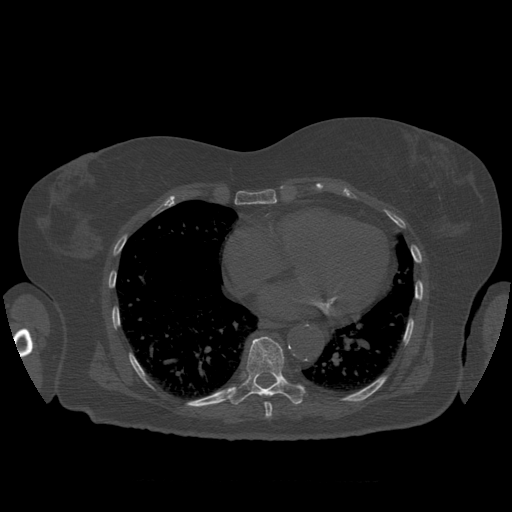
CT including the spine, one axial slice; position 363 of 399 along the scan axis; reconstruction kernel STANDARD; bone window (W 1800 / L 400 HU); 1.25 mm slice thickness; 512 × 512 image matrix, field of view 404 × 404 mm. Patient age 81 years. From the clinical record (not read from this slice): primary cancer: renal; vertebrae with lytic lesions (as recorded): L1.
Structures marked on this image (semi-automatic segmentation, software-assisted and operator-edited):
- T8 vertebra: bounding box <265,402,273,419> (left, top, right, bottom; pixels)
- T9 vertebra: <228,337,303,405>